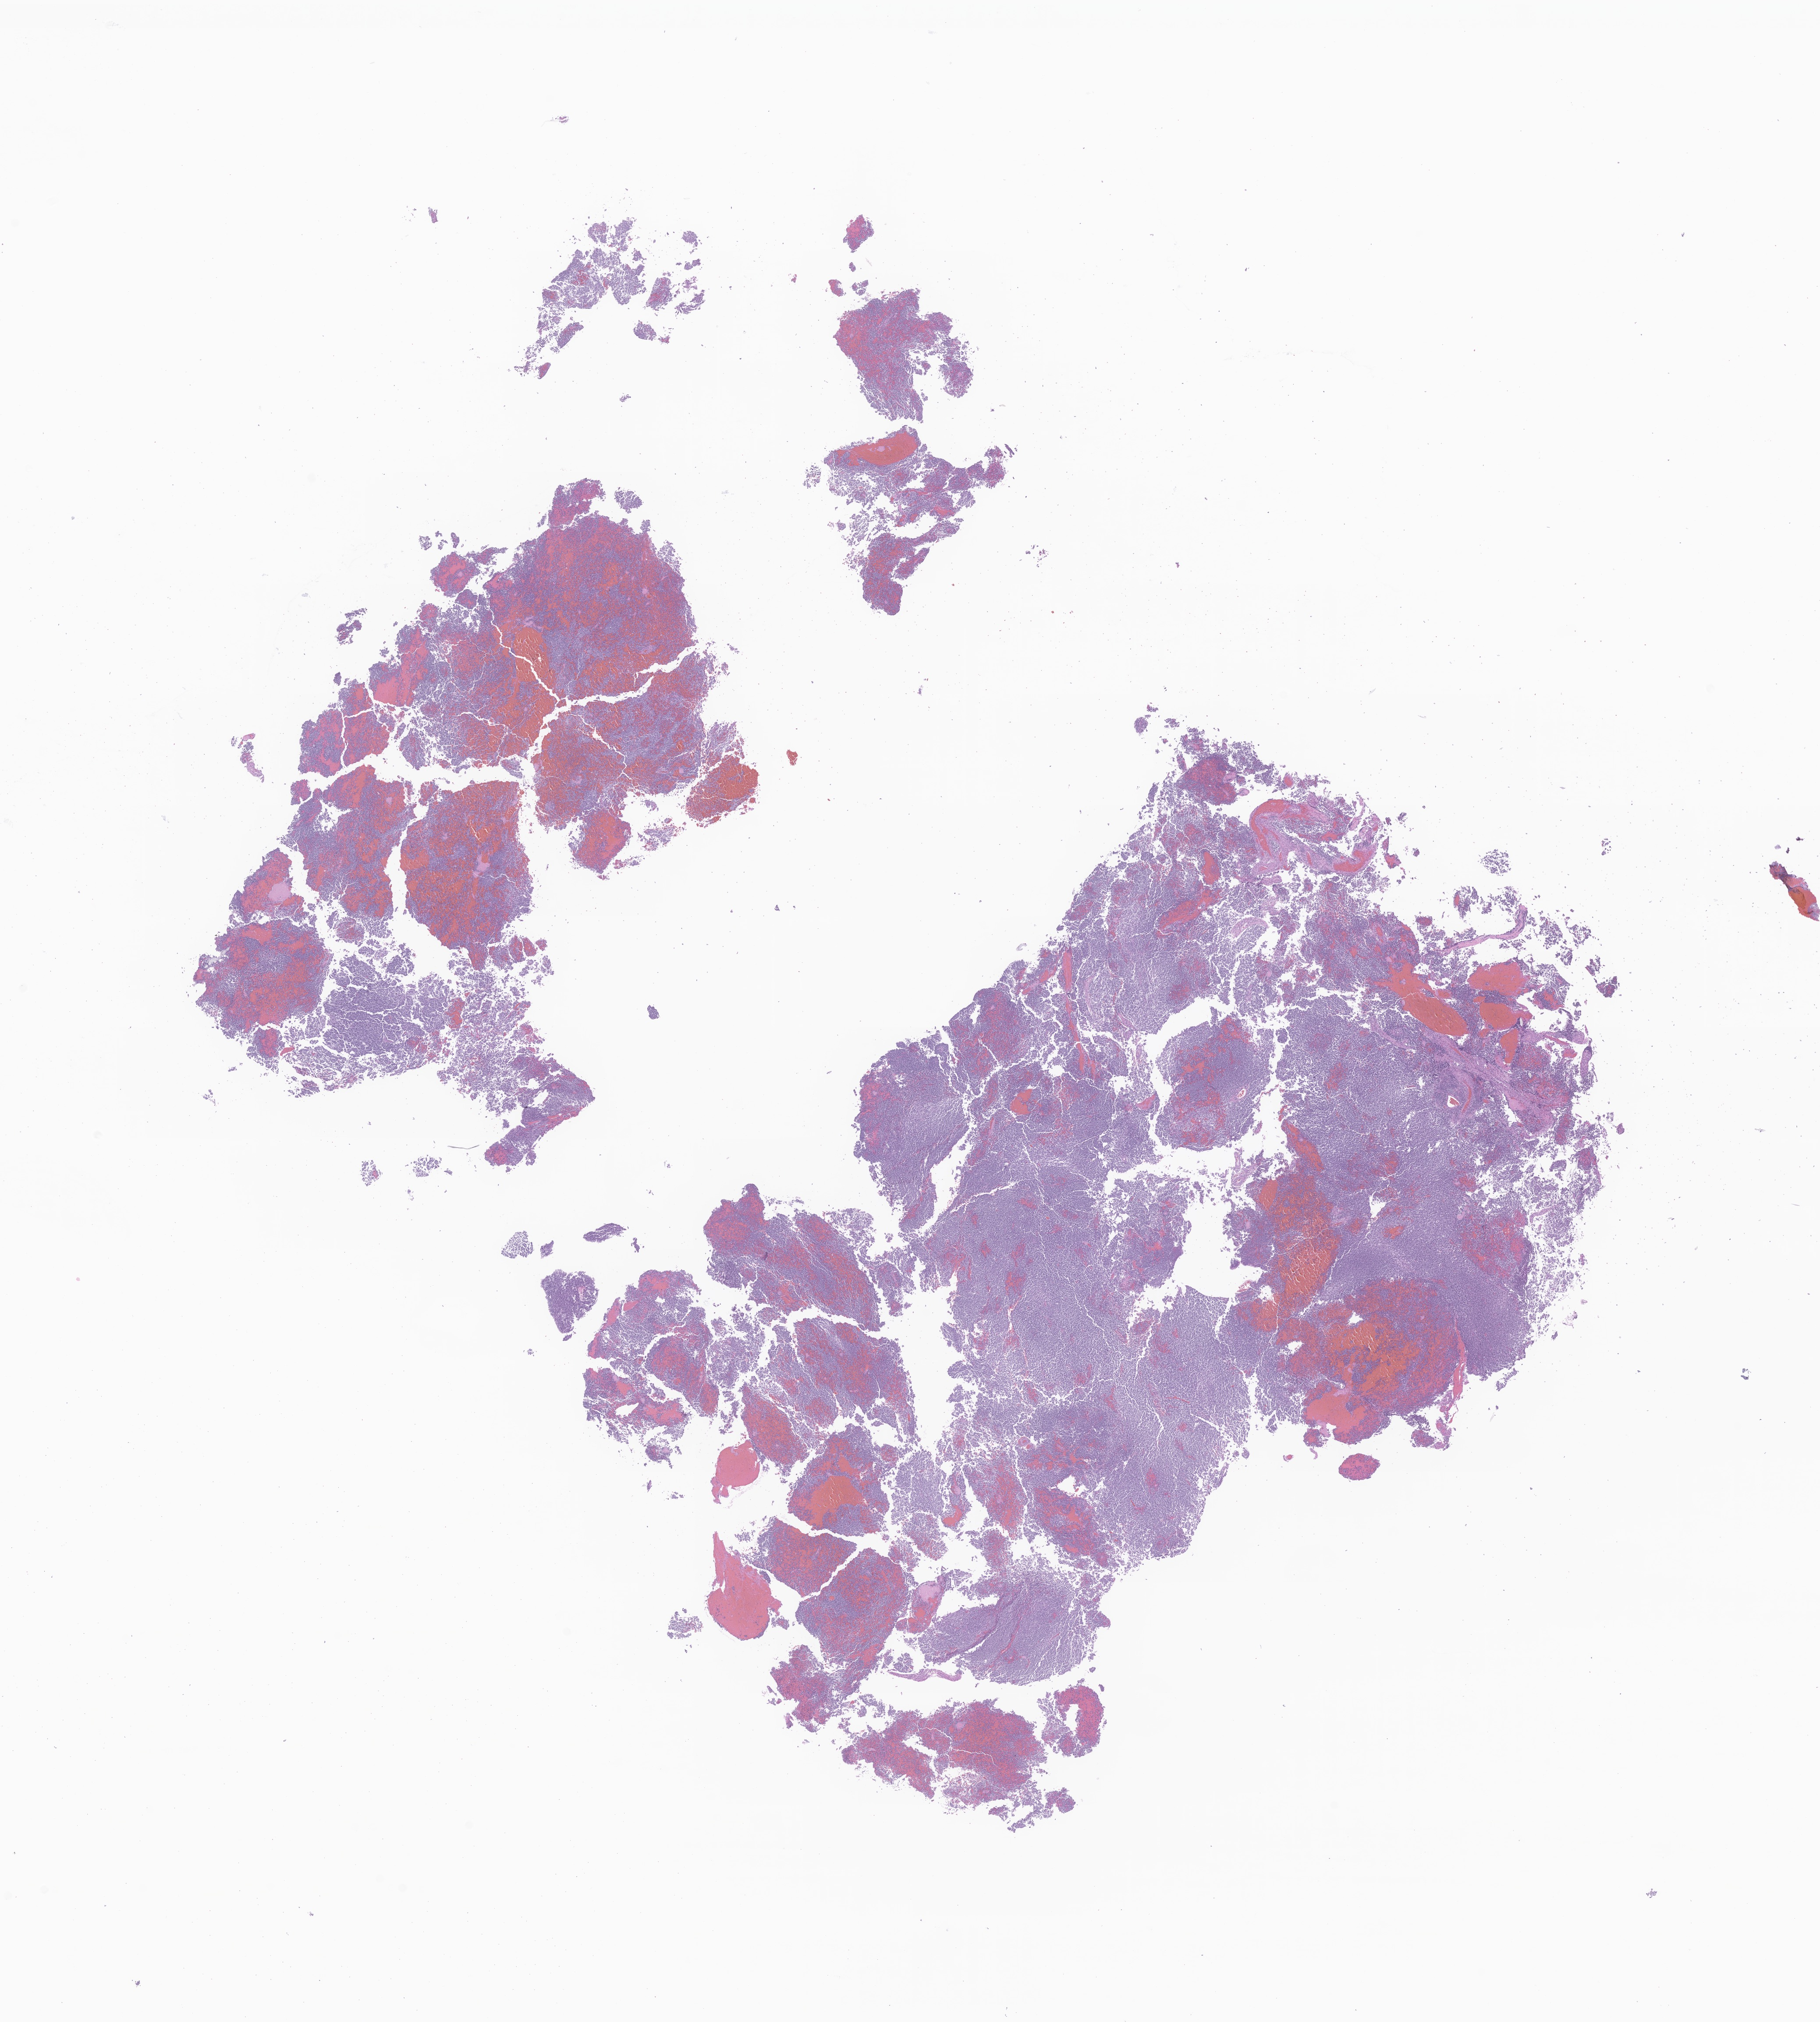
Digitized hematoxylin and eosin (H&E)-stained section of tumor tissue from the brain, shown as a low-resolution overview of the whole scanned area (about 17.5 x 19.4 mm); formalin-fixed, paraffin-embedded (FFPE) tissue. Male patient, age 51 months (4 years 3 months).
- diagnosis (ICD-O-3 morphology term): Medulloblastoma, NOS